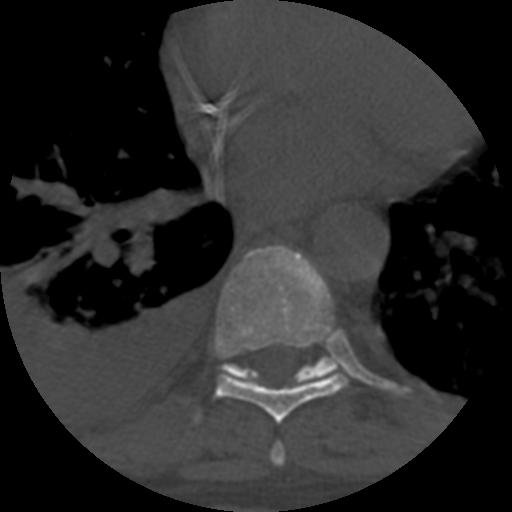
CT including the spine, one axial slice; position 392 of 708 along the scan axis; reconstruction kernel STANDARD; one of 3 acquisitions stored at this slice position; bone window (W 1800 / L 400 HU); 1.25 mm slice thickness; 512 × 512 image matrix, field of view 160 × 160 mm. Patient age 55 years. From the clinical record (not read from this slice): primary cancer: colon; vertebrae with lytic lesions (as recorded): T12, L1, L5.
Structures marked on this image (semi-automatically segmented with operator editing):
- T7 vertebra: bounding box [x1, y1, x2, y2] px = [270, 444, 286, 466]
- T8 vertebra: [215, 246, 349, 424]
- T9 vertebra: [221, 357, 338, 384]